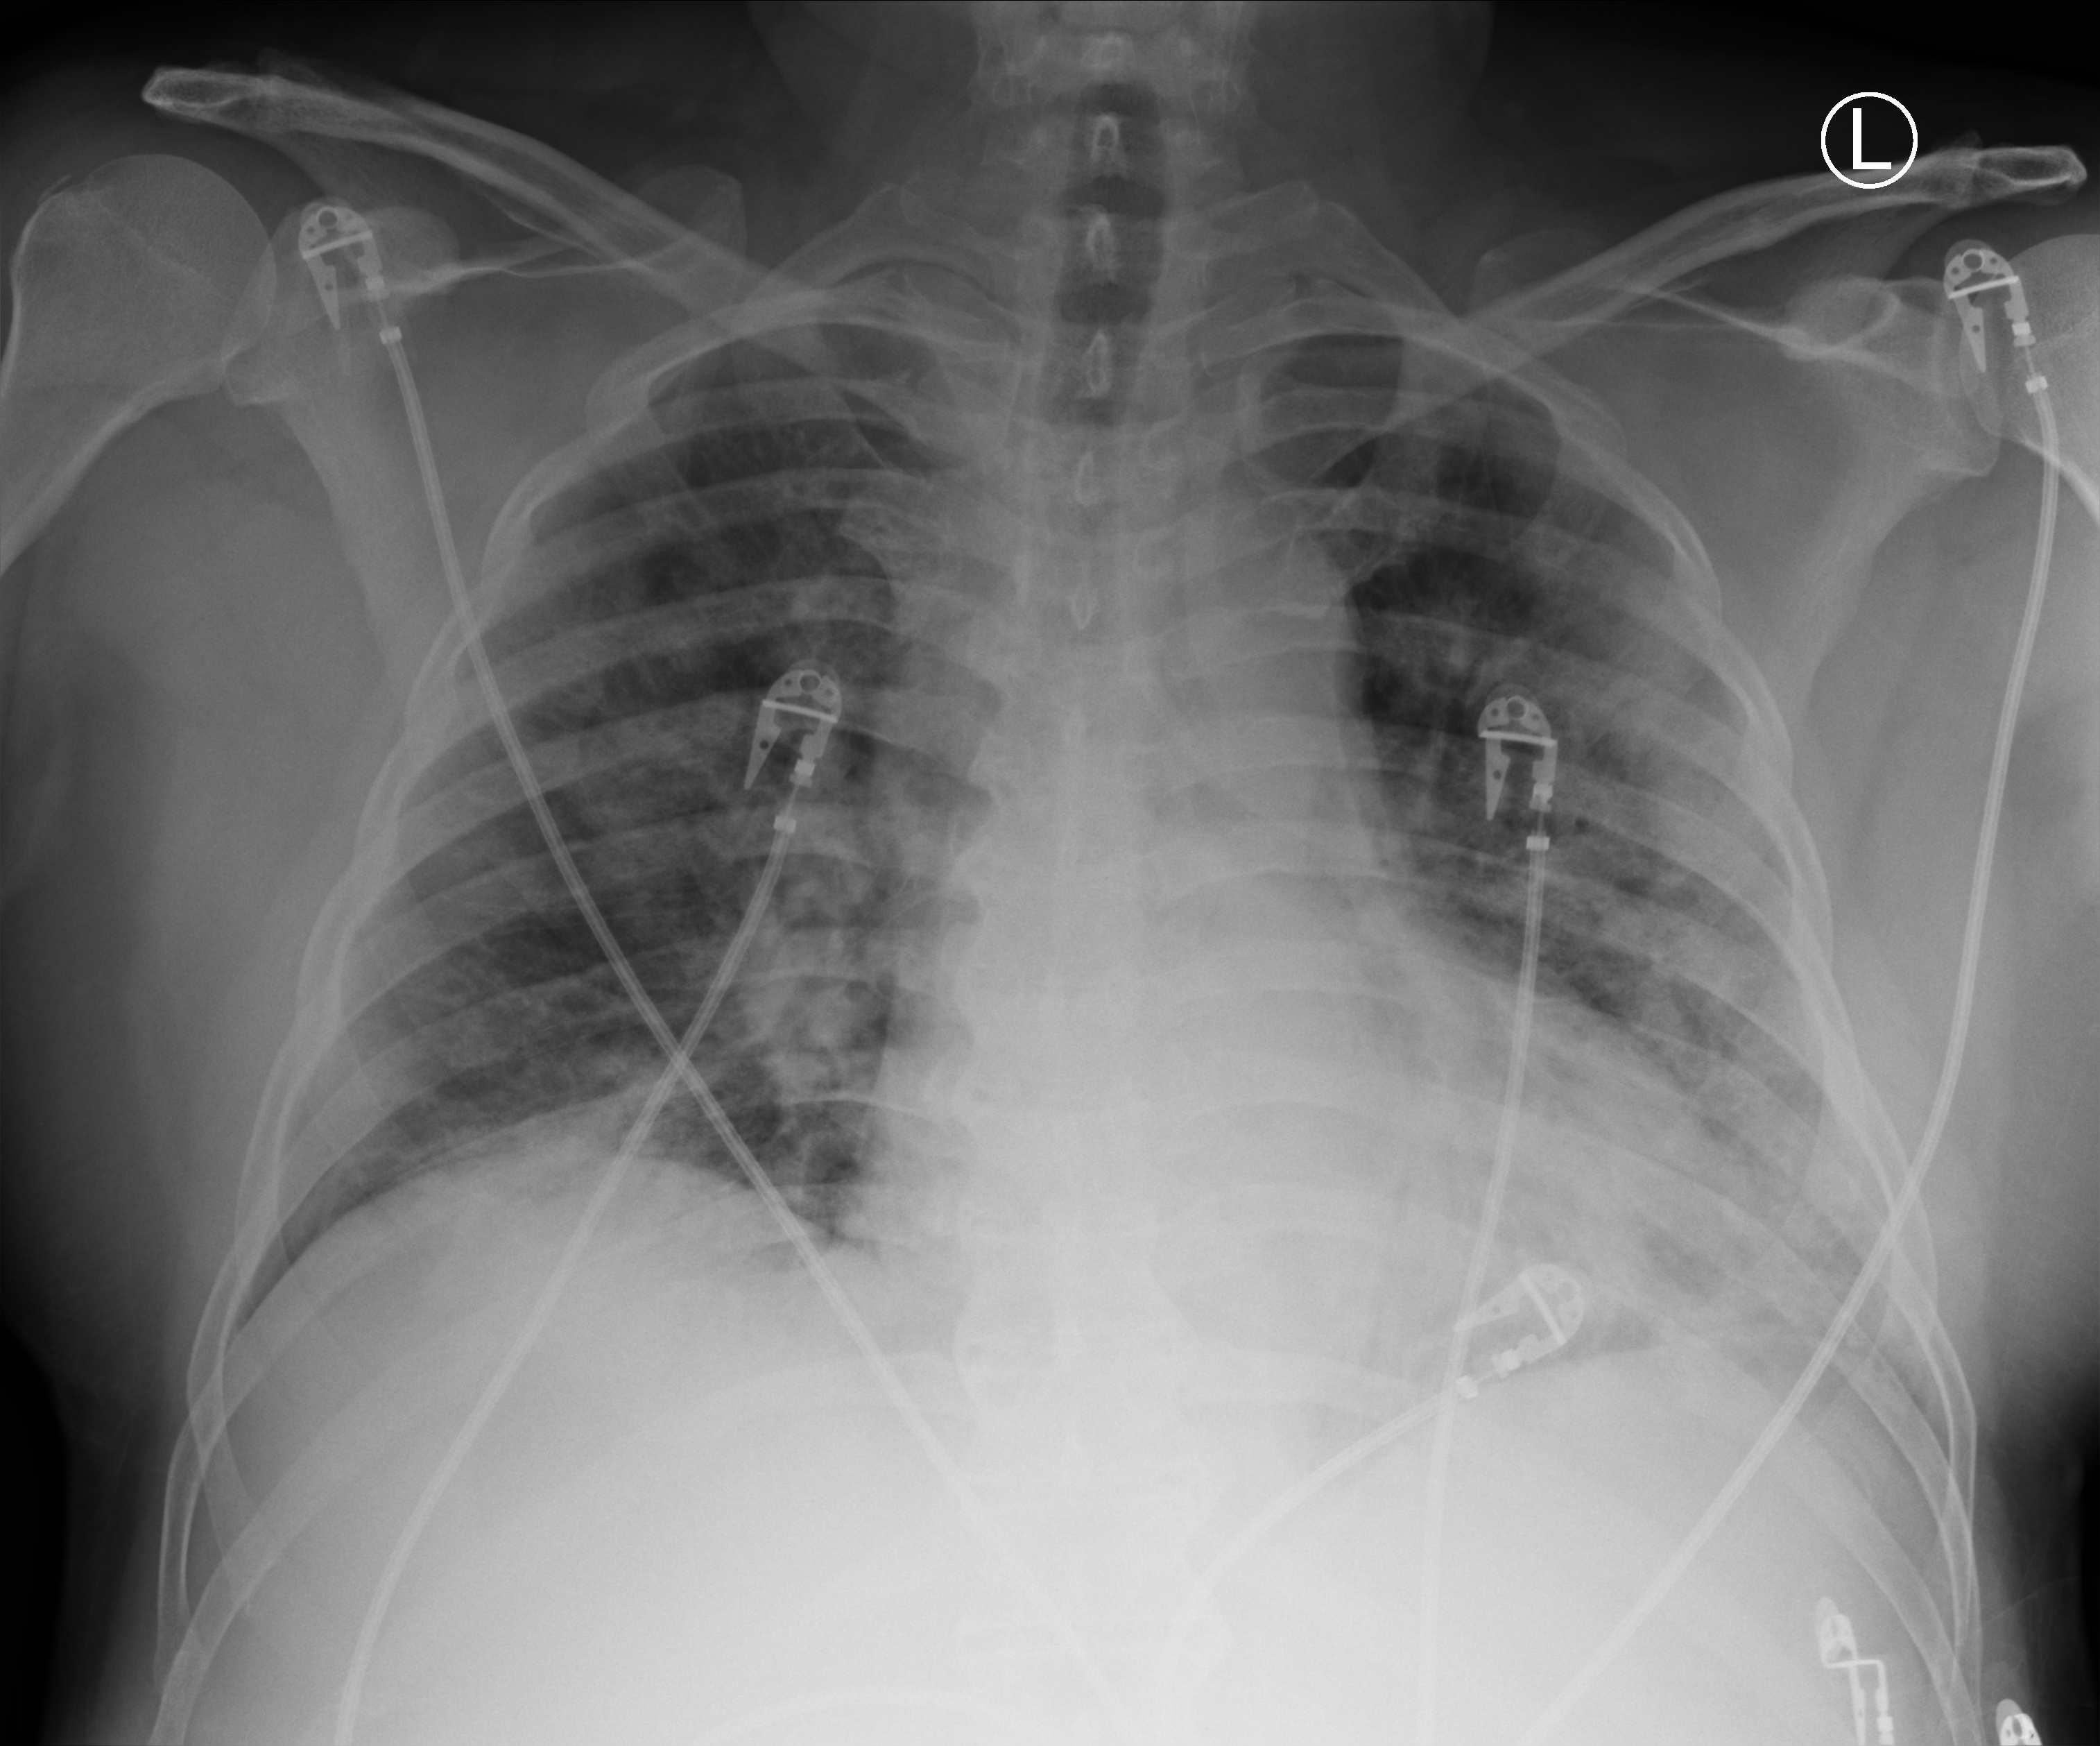
Bedside chest radiograph (computed radiography); anteroposterior (AP) projection. Male patient hospitalised with COVID-19, age 18–59 years.
From the hospital-stay record, not from the radiograph (when in the stay this image was taken is not recorded): mechanically ventilated during this hospital stay: yes; smoking status (admission record): never; admitted to intensive care during this hospital stay: yes.